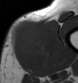
MRI of an extremity soft-tissue mass, one axial slice; position 13 of 43 along the scan axis; MR volume resampled by the dataset authors to the PET/CT grid (not the native acquisition matrix); 3.27 mm slice thickness; 78 × 83 image matrix. Male patient. From the clinical record (not read from this slice): histological type: pleiomorphic leiomyosarcoma; grade: high; site of the primary tumour: left thigh.
Structures marked on this image (expert contour drawn on MRI and transferred to this co-registered scan by the dataset authors):
- gross tumour volume including surrounding oedema: bounding box [x1, y1, x2, y2] px = [11, 19, 58, 66]
- gross tumour volume (mass): [11, 21, 55, 66]